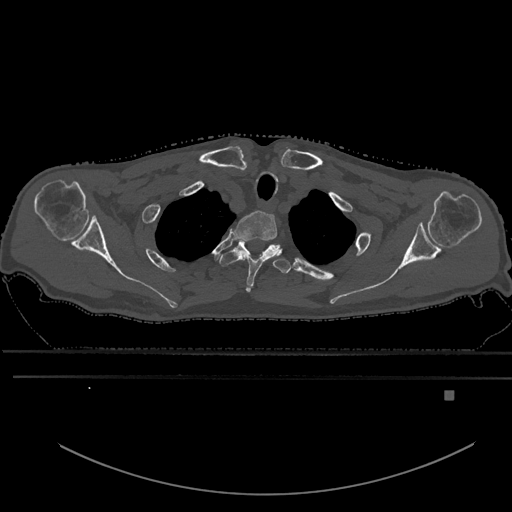
CT including the spine, one axial slice; position 515 of 969 along the scan axis; bone window (W 1800 / L 400 HU); 0.5 mm slice thickness; 512 × 512 image matrix, field of view 456 × 456 mm. Male patient, age 82 years. Case-level facts recorded for this patient, not image findings: primary cancer: prostate.
Outlined on this slice (semi-automatically segmented with operator editing):
- T1 vertebra: bounding box [x1, y1, x2, y2] px = [234, 211, 279, 293]
- T2 vertebra: [219, 239, 288, 273]